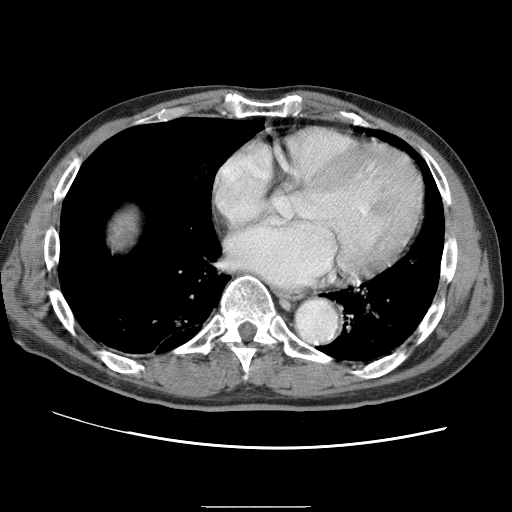
Contrast-enhanced abdominal CT (liver protocol), one axial slice; one of 2 acquisitions stored at this slice position; soft-tissue window (W 400 / L 40 HU); 2.5 mm slice thickness; 512 × 512 image matrix, field of view 360 × 360 mm. Case-level facts recorded for this patient, not image findings: diagnosis: hepatocellular carcinoma (patient treated with transarterial chemoembolisation; whether this scan precedes or follows treatment is not stated here); TNM stage (as recorded): Stage-II; Child-Pugh class: A; tumour differentiation: well differentiated; tumour size: 2 cm.
Annotated regions visible in this slice (semi-automatically segmented with operator editing):
- liver parenchyma outside the tumour (the mass and vessels are separate outlines, so this box may not span the whole liver): bounding box (x1, y1, x2, y2) in pixels: (92, 180, 164, 266)
- mass: (93, 182, 148, 265)